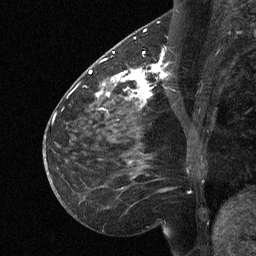
Breast MRI (dynamic contrast-enhanced), one sagittal slice; slice 26 of 64 in the series (ordered by position); dynamic contrast-enhanced study with each time point stored as its own series, time point 2 of 3 at this slice position (early post-contrast, ordered by acquisition time); 1.5 T; TE 4.8 ms, TR 27 ms; 256 × 256 image matrix. Patient: female, 51 years. Case-level facts recorded for this patient, not image findings: setting: breast cancer imaged before/during neoadjuvant chemotherapy; receptor status: HR-positive, HER2-negative.
Annotated regions visible in this slice (semi-automatic segmentation, software-assisted and operator-edited):
- analysis volume of interest (the breast-tissue region the enhancement analysis was run in; not a lesion): bounding box [x1, y1, x2, y2] px = [112, 46, 169, 106]
- tumour enhancement mask (voxels above the 90 % enhancement threshold inside the analysis volume of interest): [112, 52, 169, 106]